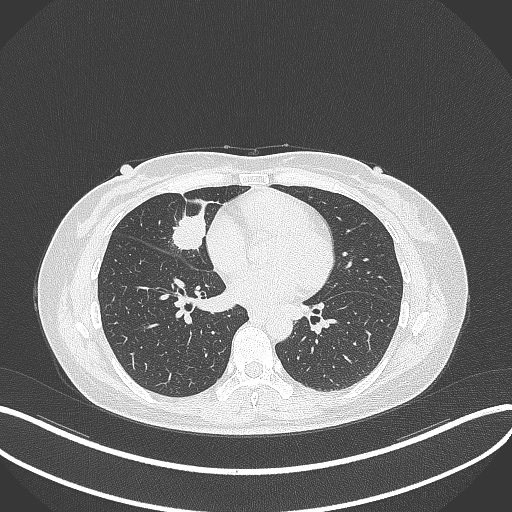
Chest CT, one axial slice; position 126 of 284 along the scan axis; reconstruction kernel B70f; lung window (W 1500 / L -600 HU); 1 mm slice thickness; 512 × 512 image matrix, field of view 400 × 400 mm. Patient: female, 43 years. Case-level facts recorded for this patient, not image findings: clinical TNM (as recorded): T1c N3 M1; histopathological grade: G1.
Annotated regions visible in this slice (rectangle marked by the reading radiologist):
- lung tumour (recorded histology: adenocarcinoma): box from (x=169, y=202) to (x=209, y=253) px